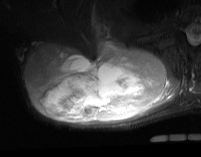
MRI of an extremity soft-tissue mass, one axial slice. Slice 40 of 74 in the series (ordered by position). STIR. MR volume resampled by the dataset authors to the PET/CT grid (not the native acquisition matrix). 3.27 mm slice thickness. 201 × 157 image matrix, field of view 196 × 153 mm. Male patient. From the clinical record (not read from this slice): histological type: pleiomorphic spindle cell undifferentiated; grade: high; site of the primary tumour: right parascapusular.
Outlined on this slice (expert contour drawn on MRI and transferred to this co-registered scan by the dataset authors):
- gross tumour volume including surrounding oedema: box from (x=26, y=38) to (x=180, y=124) px
- gross tumour volume (mass): (x=26, y=43)–(x=166, y=124)